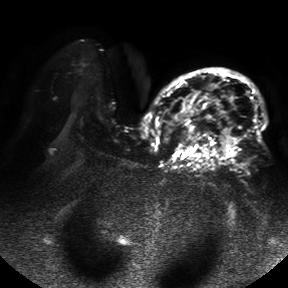
Breast MRI, one axial slice; position 30 of 50 along the scan axis; diffusion-weighted series; image 2 of 4 stored at this slice position (different b-values; order by instance number); 1.5 T; 288 × 288 image matrix, field of view 390 × 390 mm. Female patient.
Outlined on this slice (expert manual segmentation):
- tumour on diffusion-weighted imaging: bounding box [x1, y1, x2, y2] px = [167, 91, 238, 159]